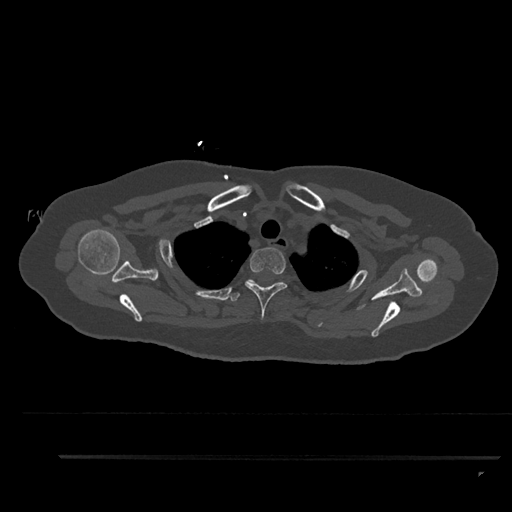
CT including the spine, one axial slice. Slice 716 of 797 in the series (ordered by position). 120 kVp. Bone window (W 1800 / L 400 HU). 512 × 512 image matrix, field of view 408 × 408 mm. Female patient, age 44 years. From the clinical record (not read from this slice): primary cancer: renal; vertebrae with lytic lesions (as recorded): L1.
Annotated regions visible in this slice (semi-automatic segmentation, software-assisted and operator-edited):
- T2 vertebra: bounding box <245,248,287,320> (left, top, right, bottom; pixels)
- T3 vertebra: <228,279,255,301>